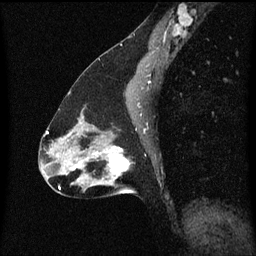
Breast MRI (dynamic contrast-enhanced), one sagittal slice; slice 33 of 60 in the series (ordered by position); dynamic contrast-enhanced series, image 2 of 3 at this slice position (ordered by acquisition); 1.5 T; TE 4.2 ms, TR 8.4 ms; 2 mm slice thickness; 256 × 256 image matrix, field of view 200 × 200 mm. Female patient, age 47 years.
Annotated regions visible in this slice (semi-automatically segmented with operator editing):
- analysis volume of interest (the breast-tissue region the enhancement analysis was run in; not a lesion): bounding box <85,136,139,195> (left, top, right, bottom; pixels)
- tumour enhancement mask (voxels above the 70 % enhancement threshold inside the analysis volume of interest): <93,146,129,179>